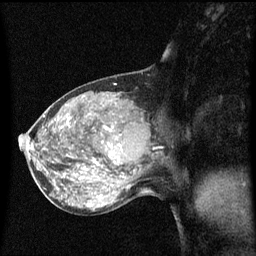
Breast MRI (dynamic contrast-enhanced), one sagittal slice; slice 28 of 60 in the series (ordered by position); dynamic contrast-enhanced series, image 2 of 3 at this slice position (ordered by acquisition); 1.5 T; TE 4.2 ms, TR 8.4 ms; 2 mm slice thickness; 256 × 256 image matrix, field of view 200 × 200 mm. Patient: female, 50 years.
Structures marked on this image (semi-automatic segmentation, software-assisted and operator-edited):
- analysis volume of interest (the breast-tissue region the enhancement analysis was run in; not a lesion): bounding box (x1, y1, x2, y2) in pixels: (100, 114, 153, 171)
- tumour enhancement mask (voxels above the 70 % enhancement threshold inside the analysis volume of interest): (105, 128, 115, 163)